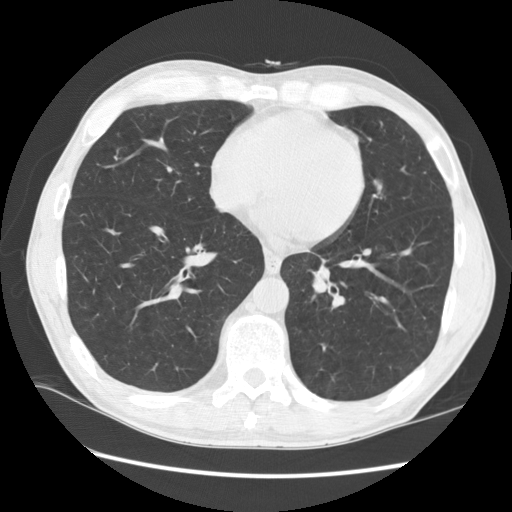
Low-dose screening chest CT, one axial slice; position 49 of 141 along the scan axis; reconstruction kernel STANDARD; 120 kVp; lung window (W 1500 / L -600 HU); 2.5 mm slice thickness; 512 × 512 image matrix, field of view 360 × 360 mm.
Outlined on this slice (outlined manually by an expert reader):
- lesion 2 (nodule, lower lobe of left lung): bounding box [x1, y1, x2, y2] px = [311, 278, 328, 295]